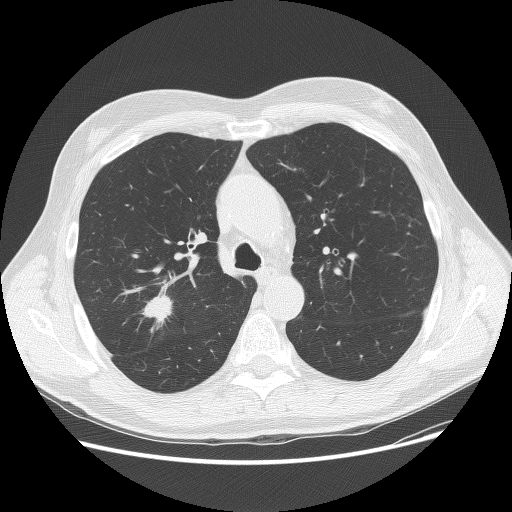
Axial slice from a low-dose chest CT screening exam, baseline screening round, lung window (W 1500 / L -600 HU), 2.5 mm slice thickness, slice 51 of 156 in the series, 512 × 512 image matrix. Male, age 70 years at enrolment. Current smoker at enrolment.
Expert reader's lesion annotation, bounding box (x1, y1, x2, y2) in pixels: (132, 281, 194, 336). The screening reader recorded 2 non-calcified nodules or masses ≥4 mm on this exam; which of them this box marks is not recorded. Official screen result: positive, change unspecified: nodule(s) >= 4 mm or enlarging nodule(s), mass(es), or other non-specific abnormalities suspicious for lung cancer. Participant outcome: lung cancer diagnosed 15 days after this screen — adenocarcinoma, NOS, right upper lobe, poorly differentiated (G3), stage IIA (AJCC 6th edition), 23 mm at pathology.